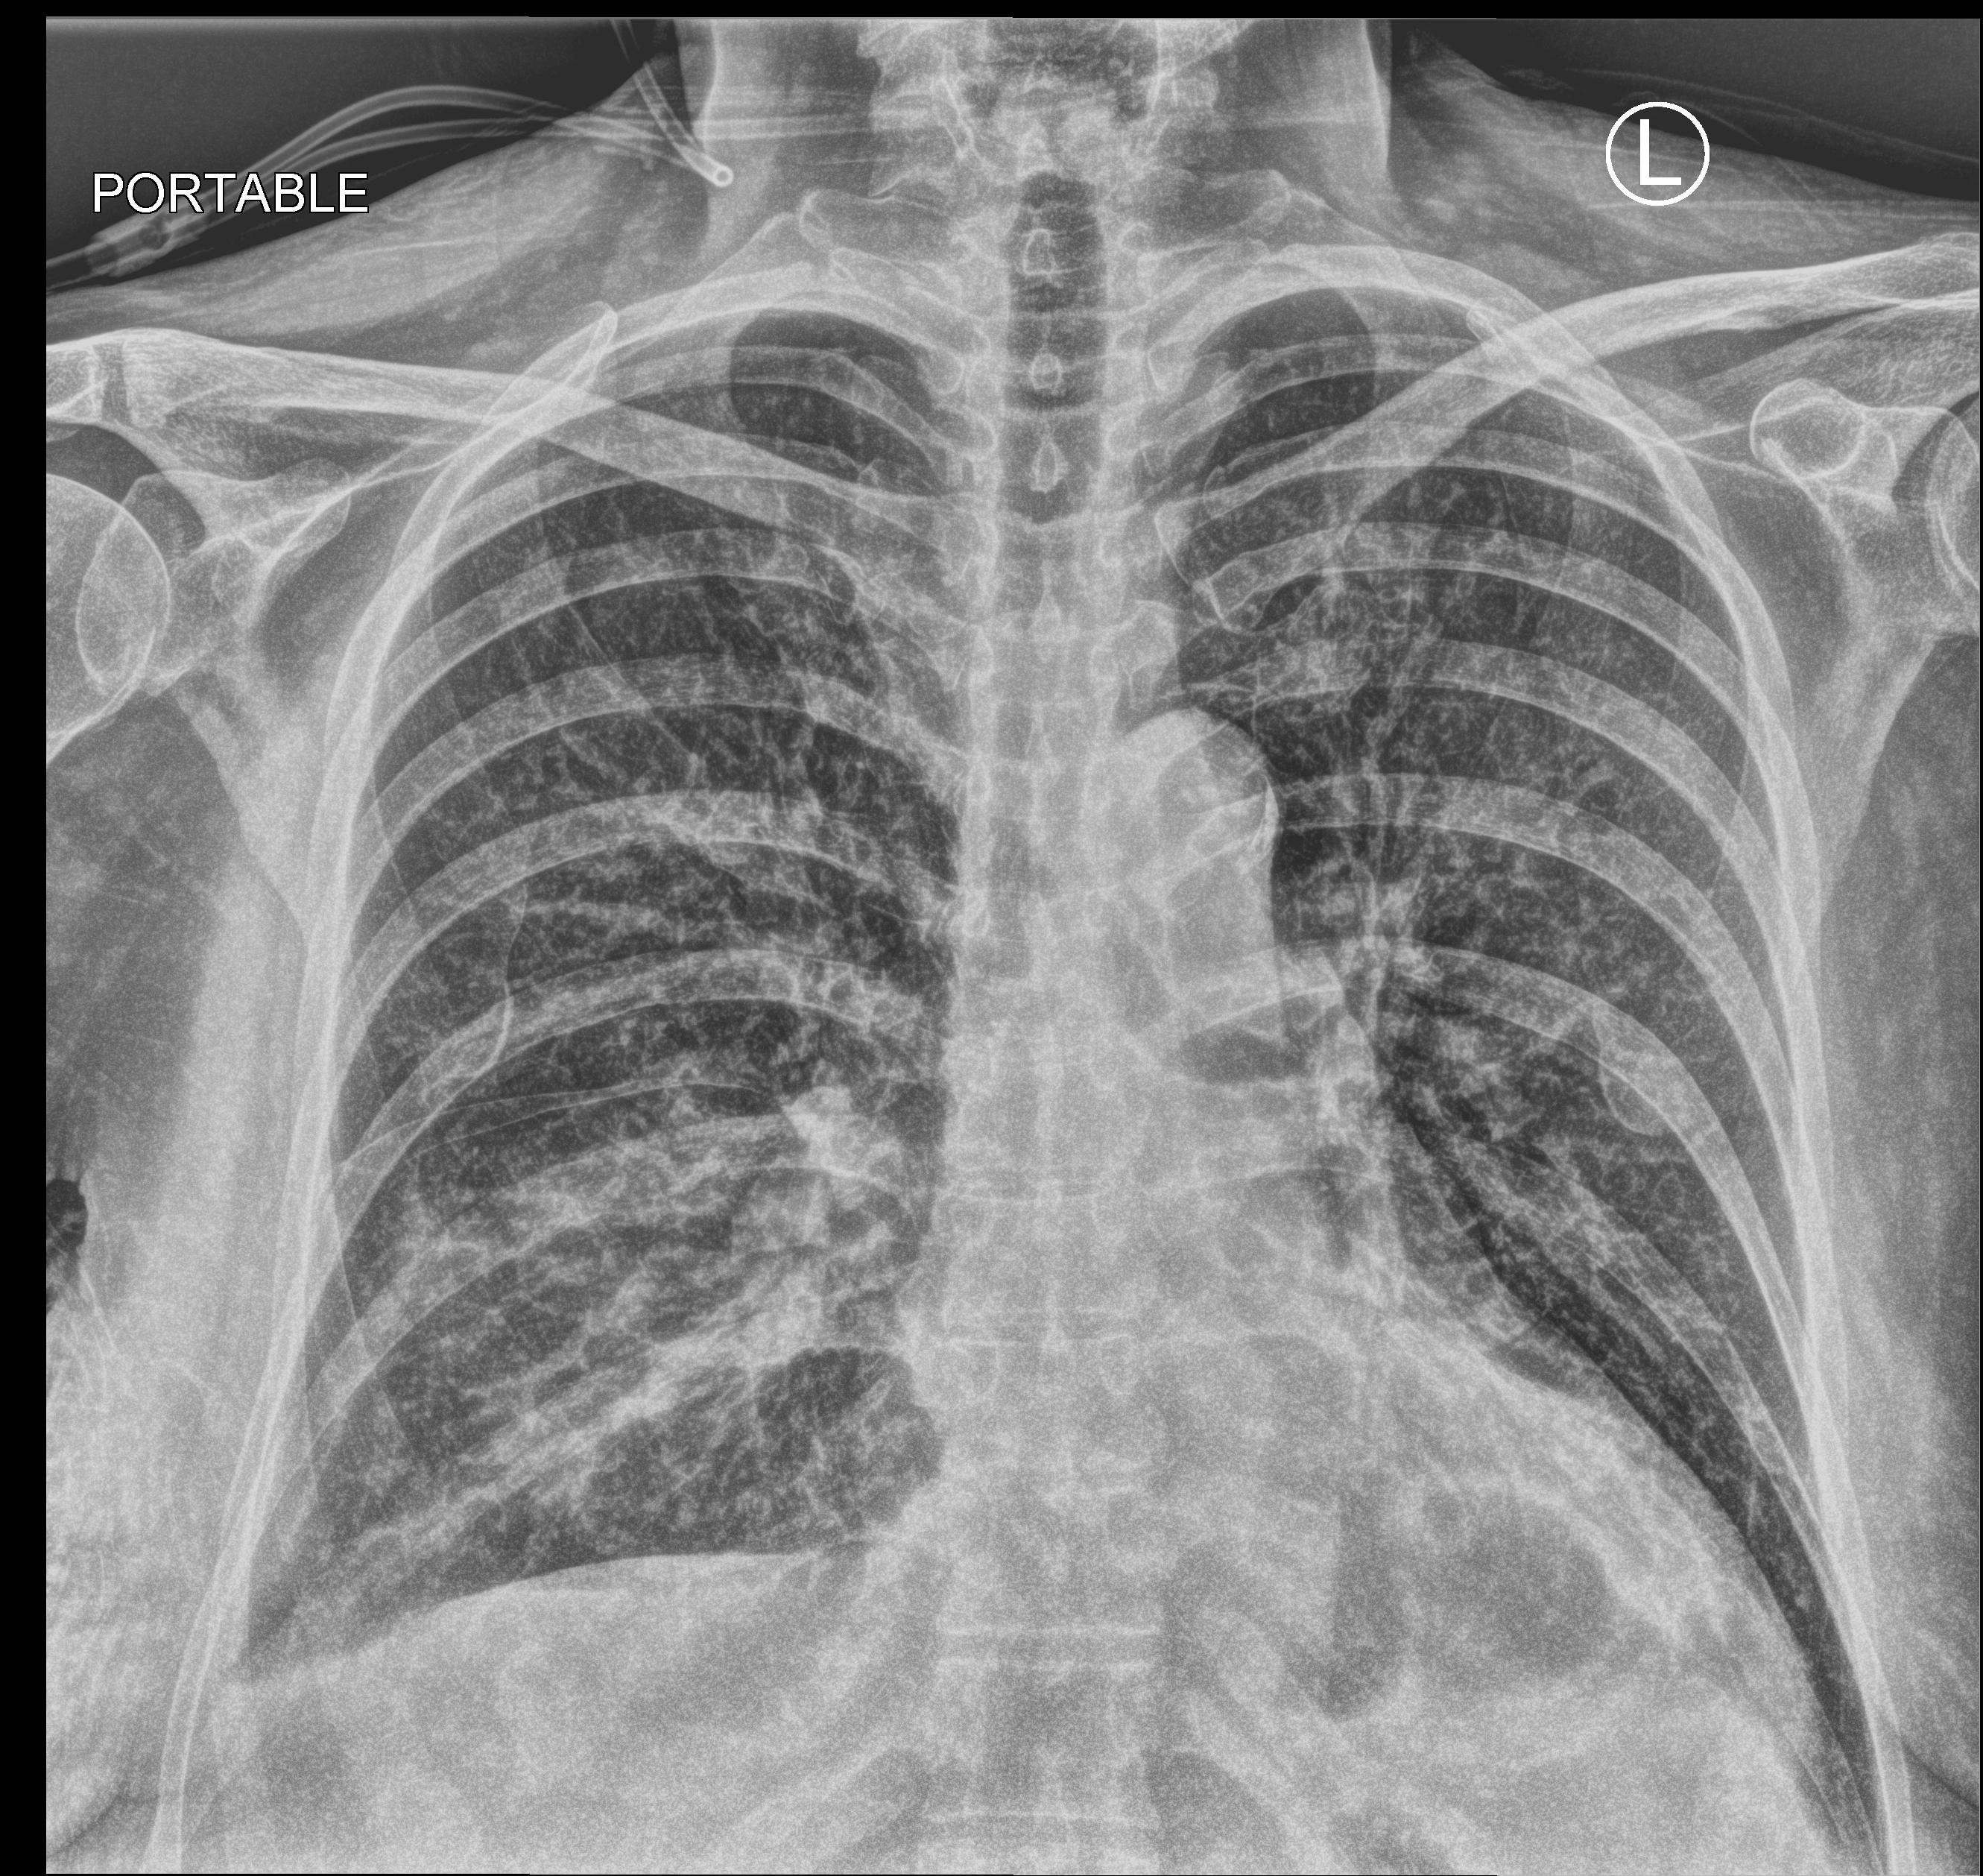
Bedside chest radiograph (computed radiography); anteroposterior (AP) projection. Patient hospitalised with COVID-19; female, aged 18–59 years.
Admission-level facts for this patient (not findings on this image; timing relative to this image not recorded): mechanically ventilated during this hospital stay: no; length of hospital stay: 11 days.